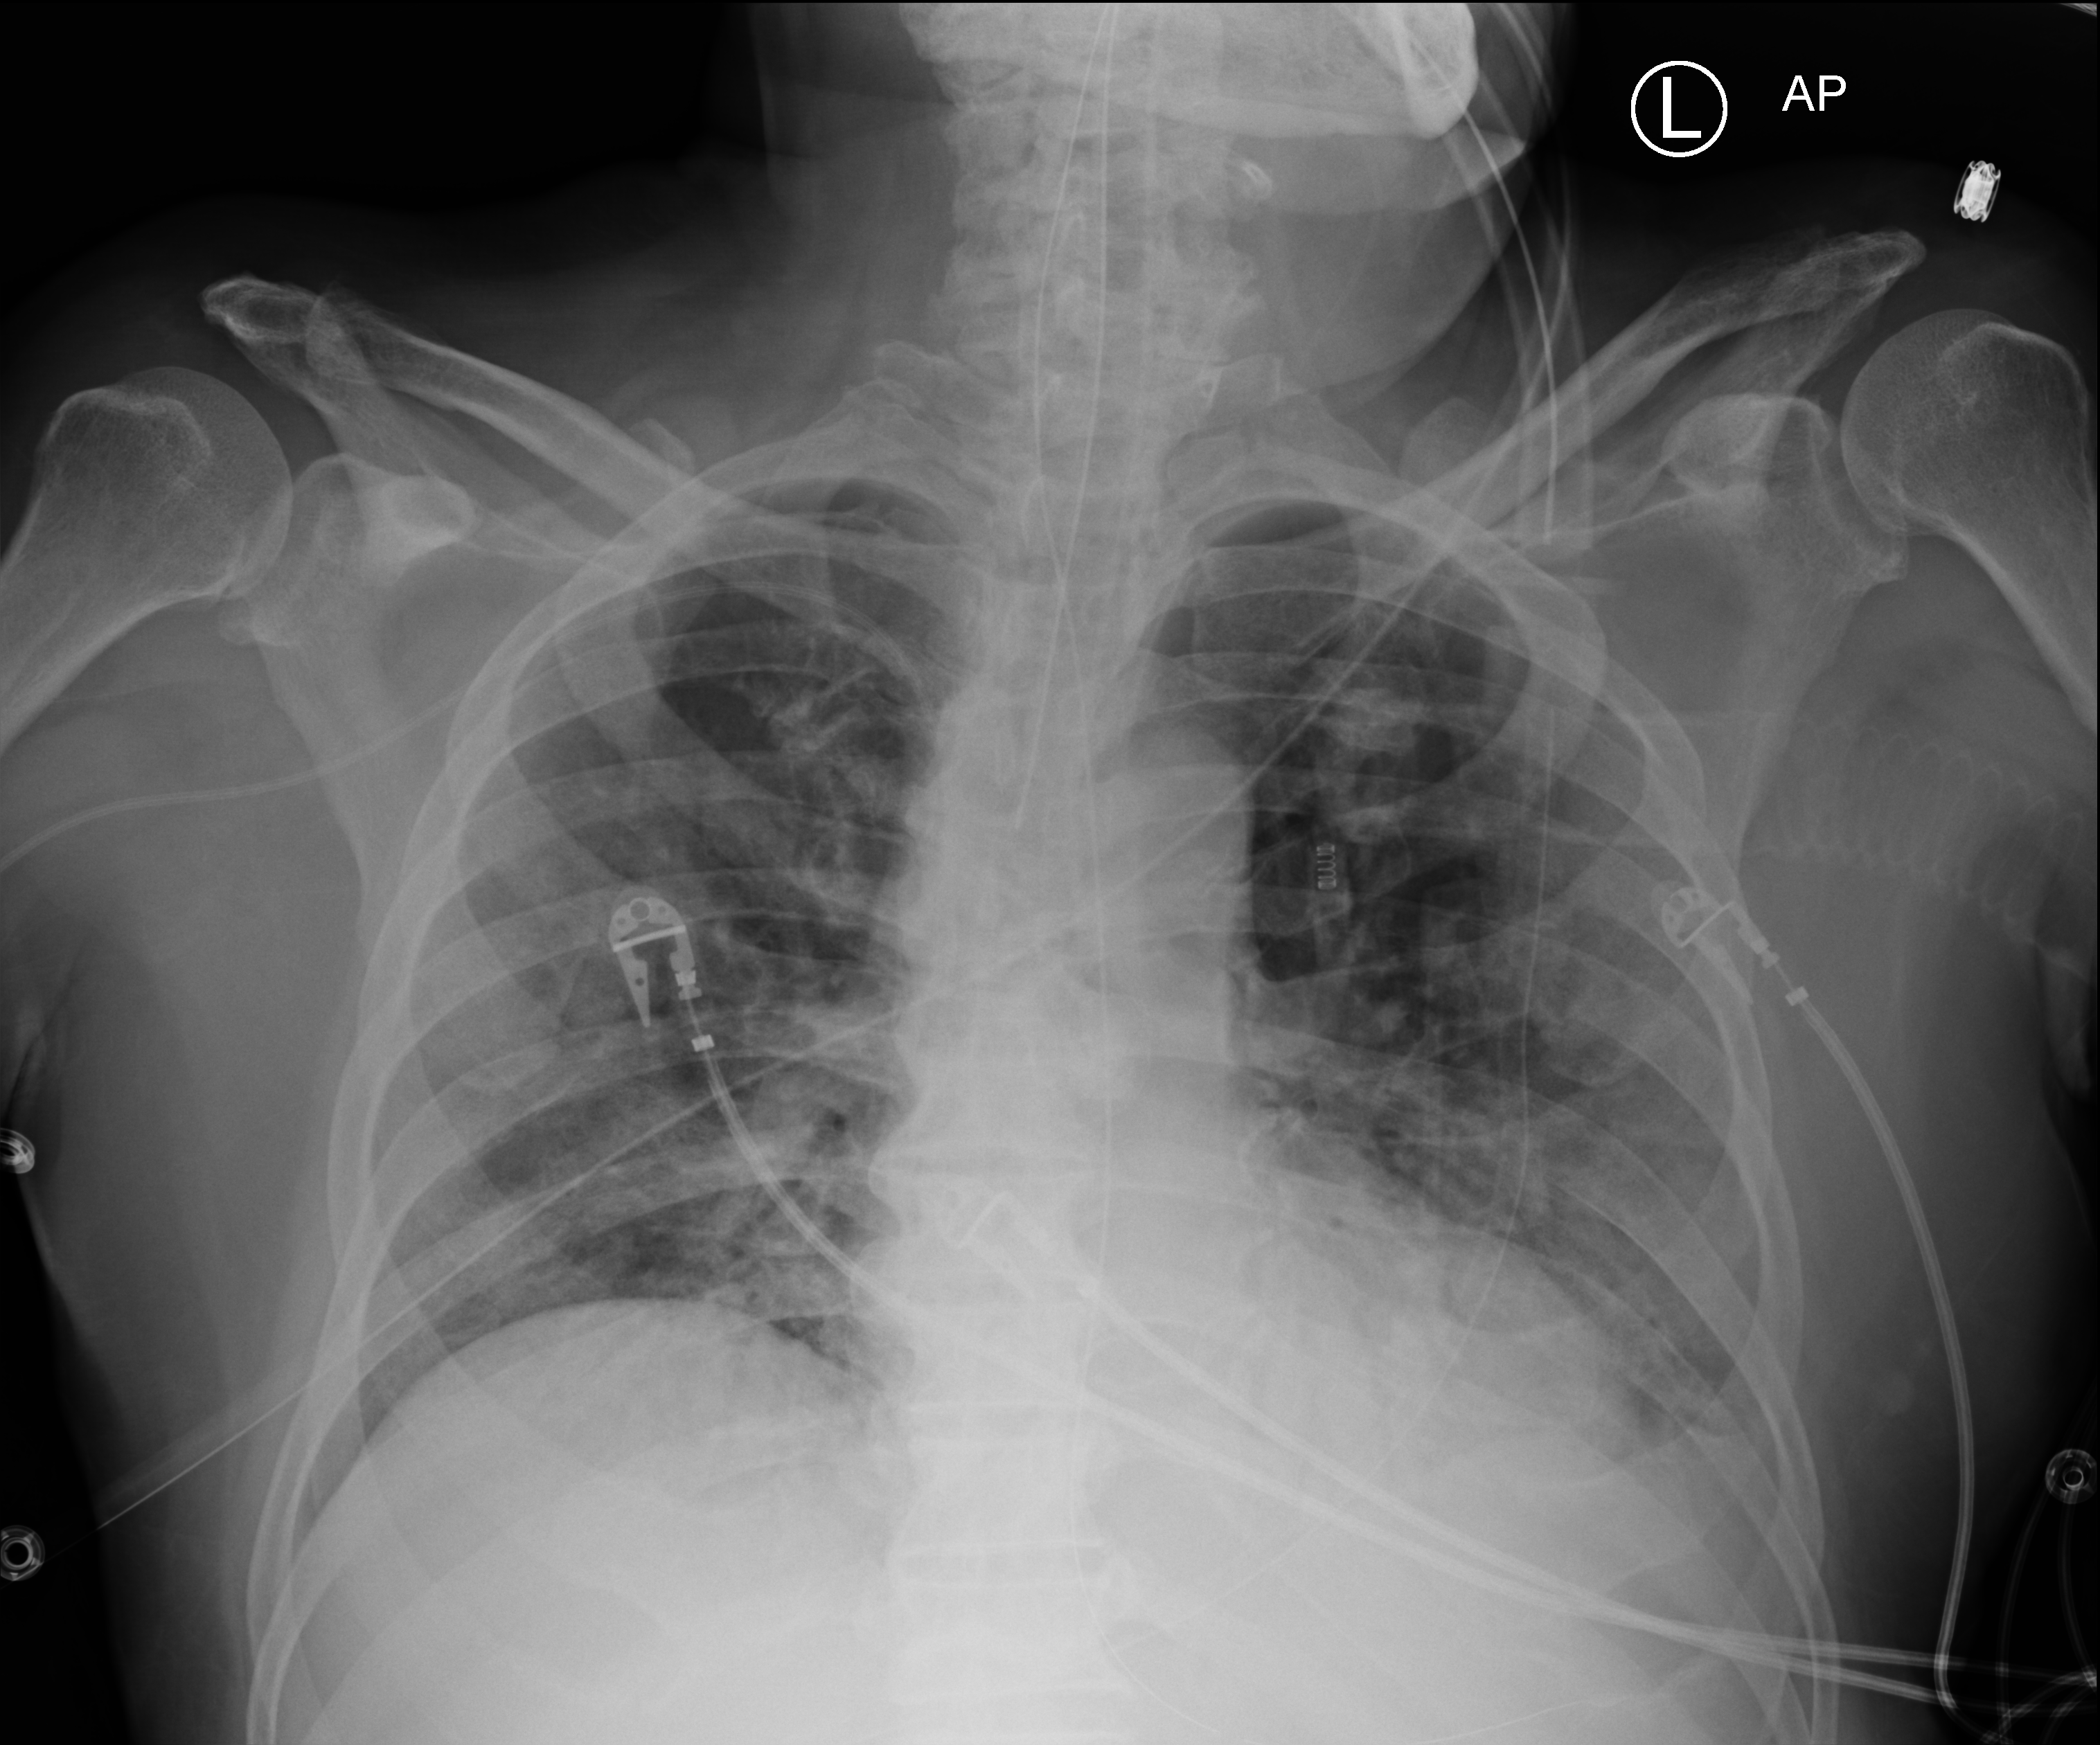
Portable chest radiograph, anteroposterior (AP) projection. Male patient hospitalised with COVID-19, age 75–90 years.
Admission-level facts for this patient (not findings on this image; timing relative to this image not recorded): mechanically ventilated during this hospital stay: yes.